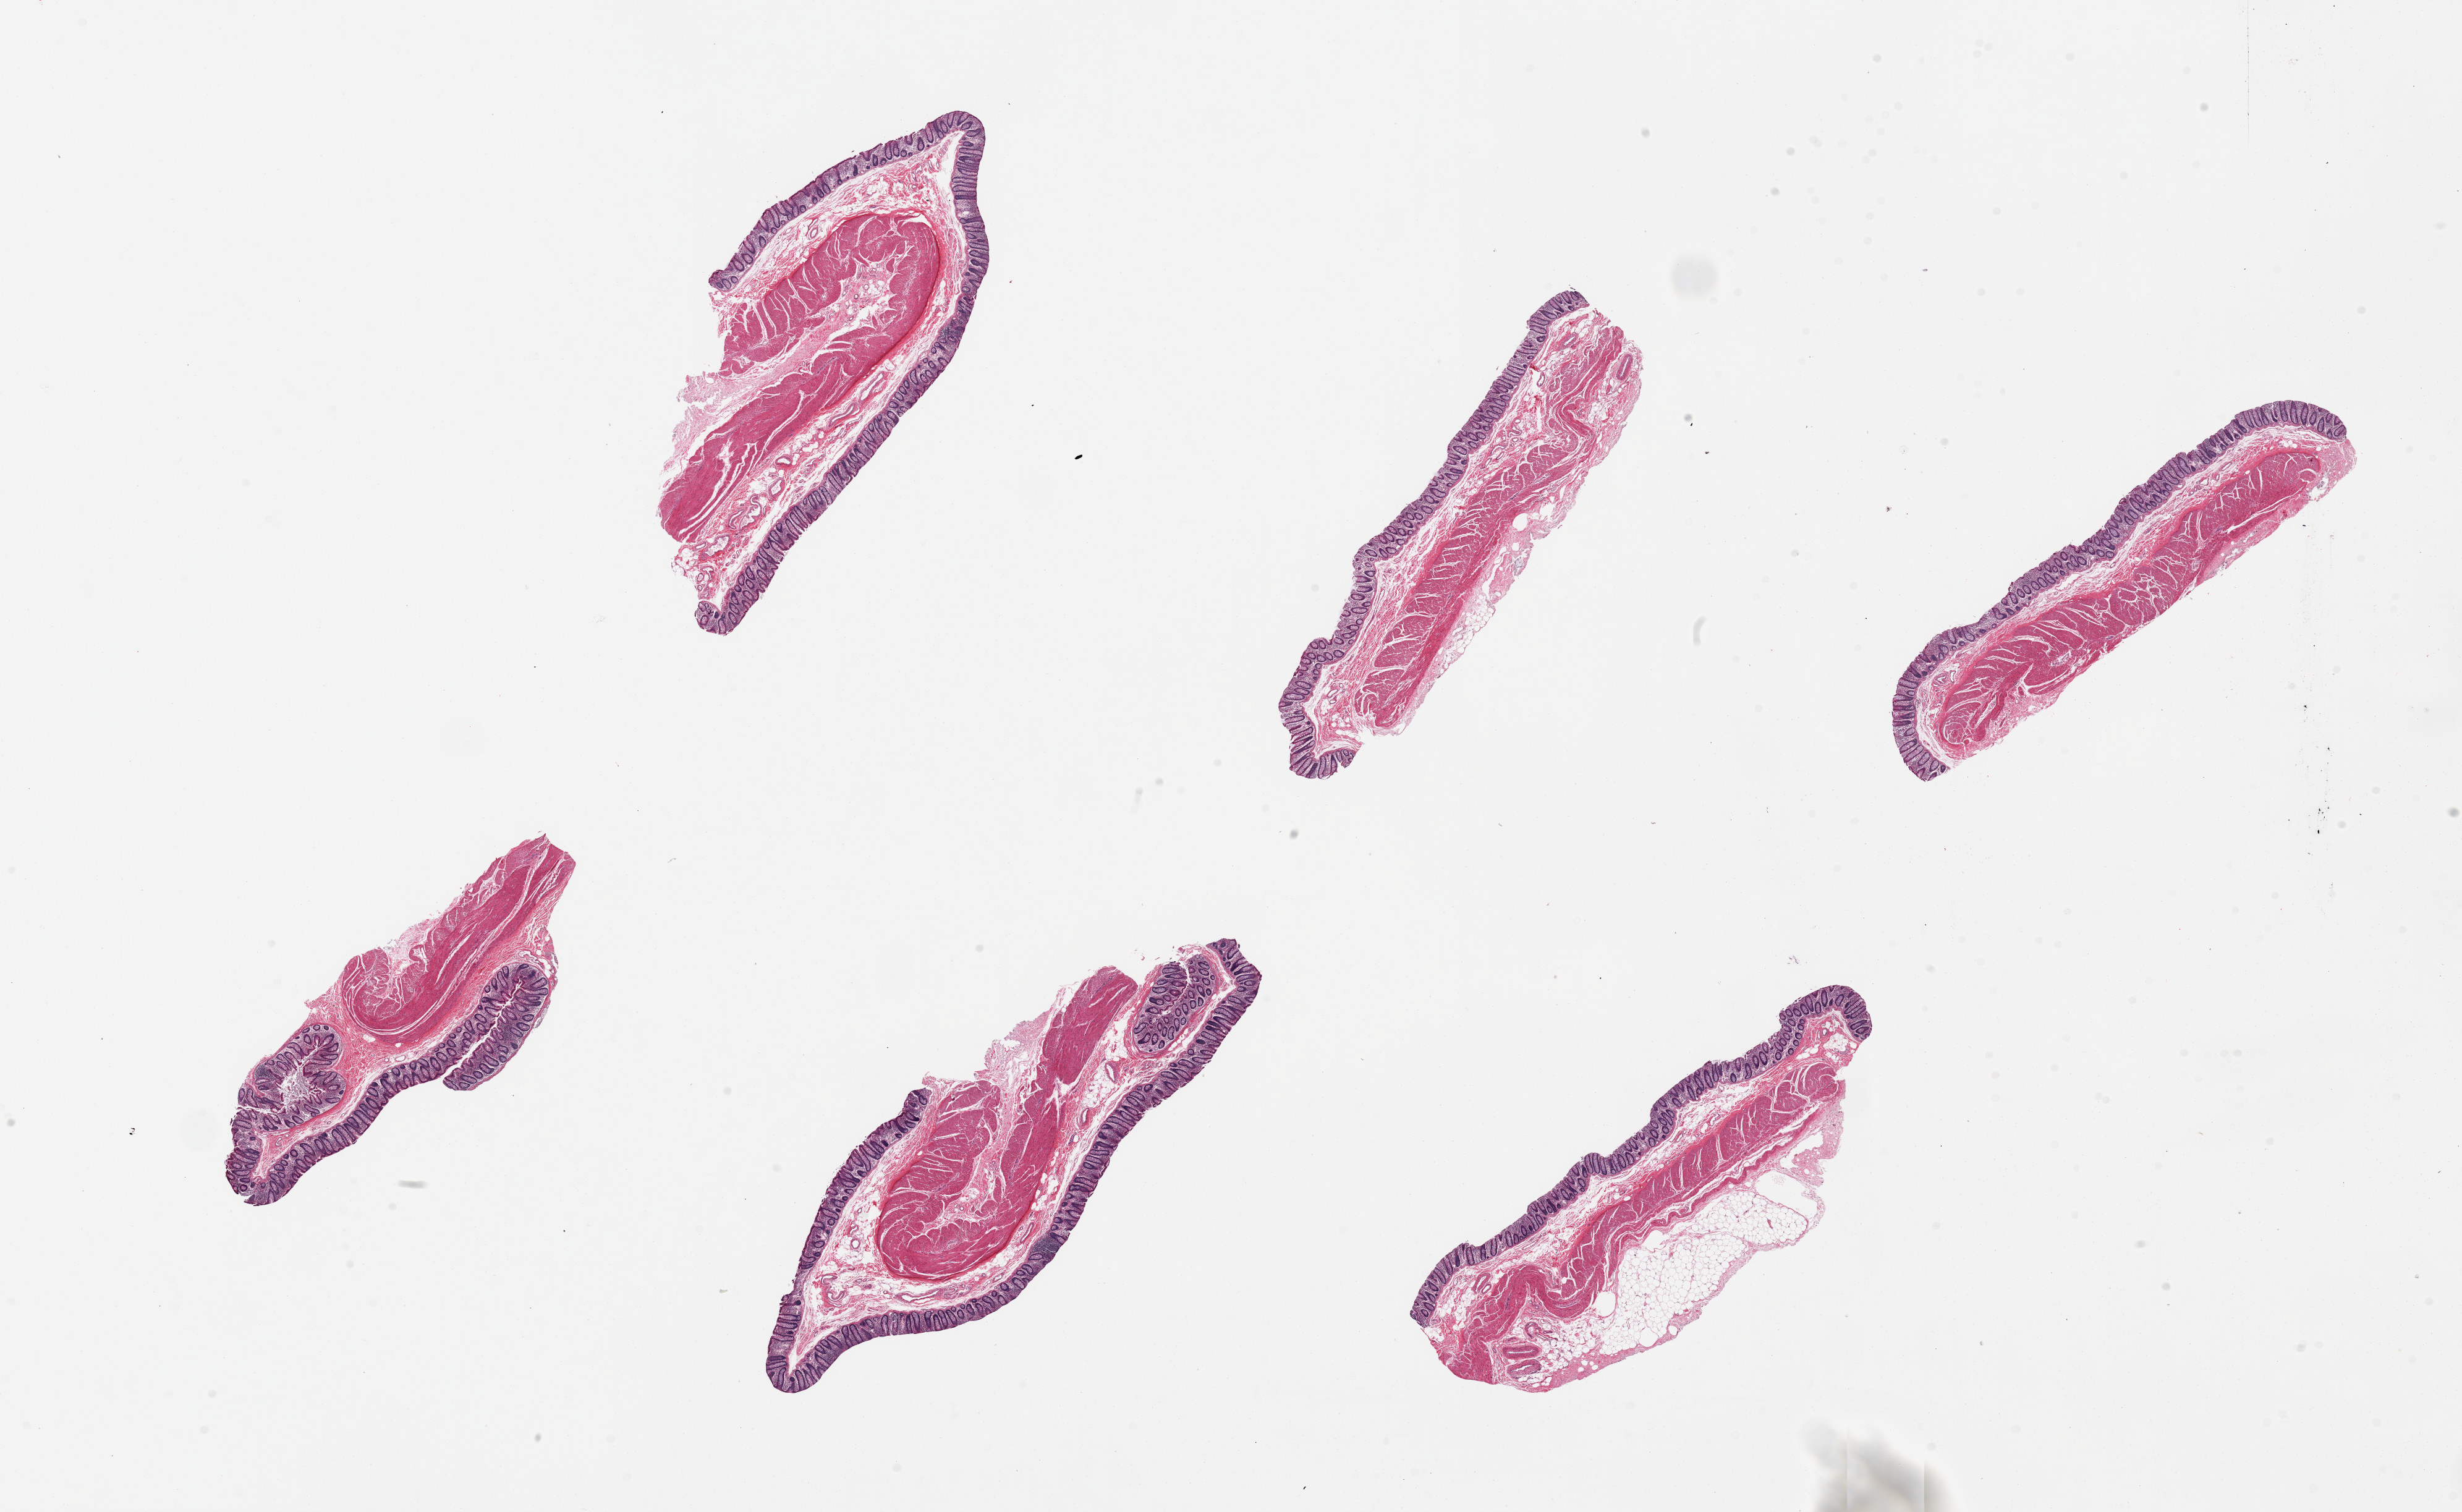
H&E whole-slide image — low-resolution overview of the scanned area, about 31.5 x 19.3 mm, PAXgene-fixed paraffin-embedded (PFPE) section, target tissue: transverse colon, donor tissue sample. Donor sex: male.
Reviewer comment on this tissue sample: 1 piece; comparable to 25 block.